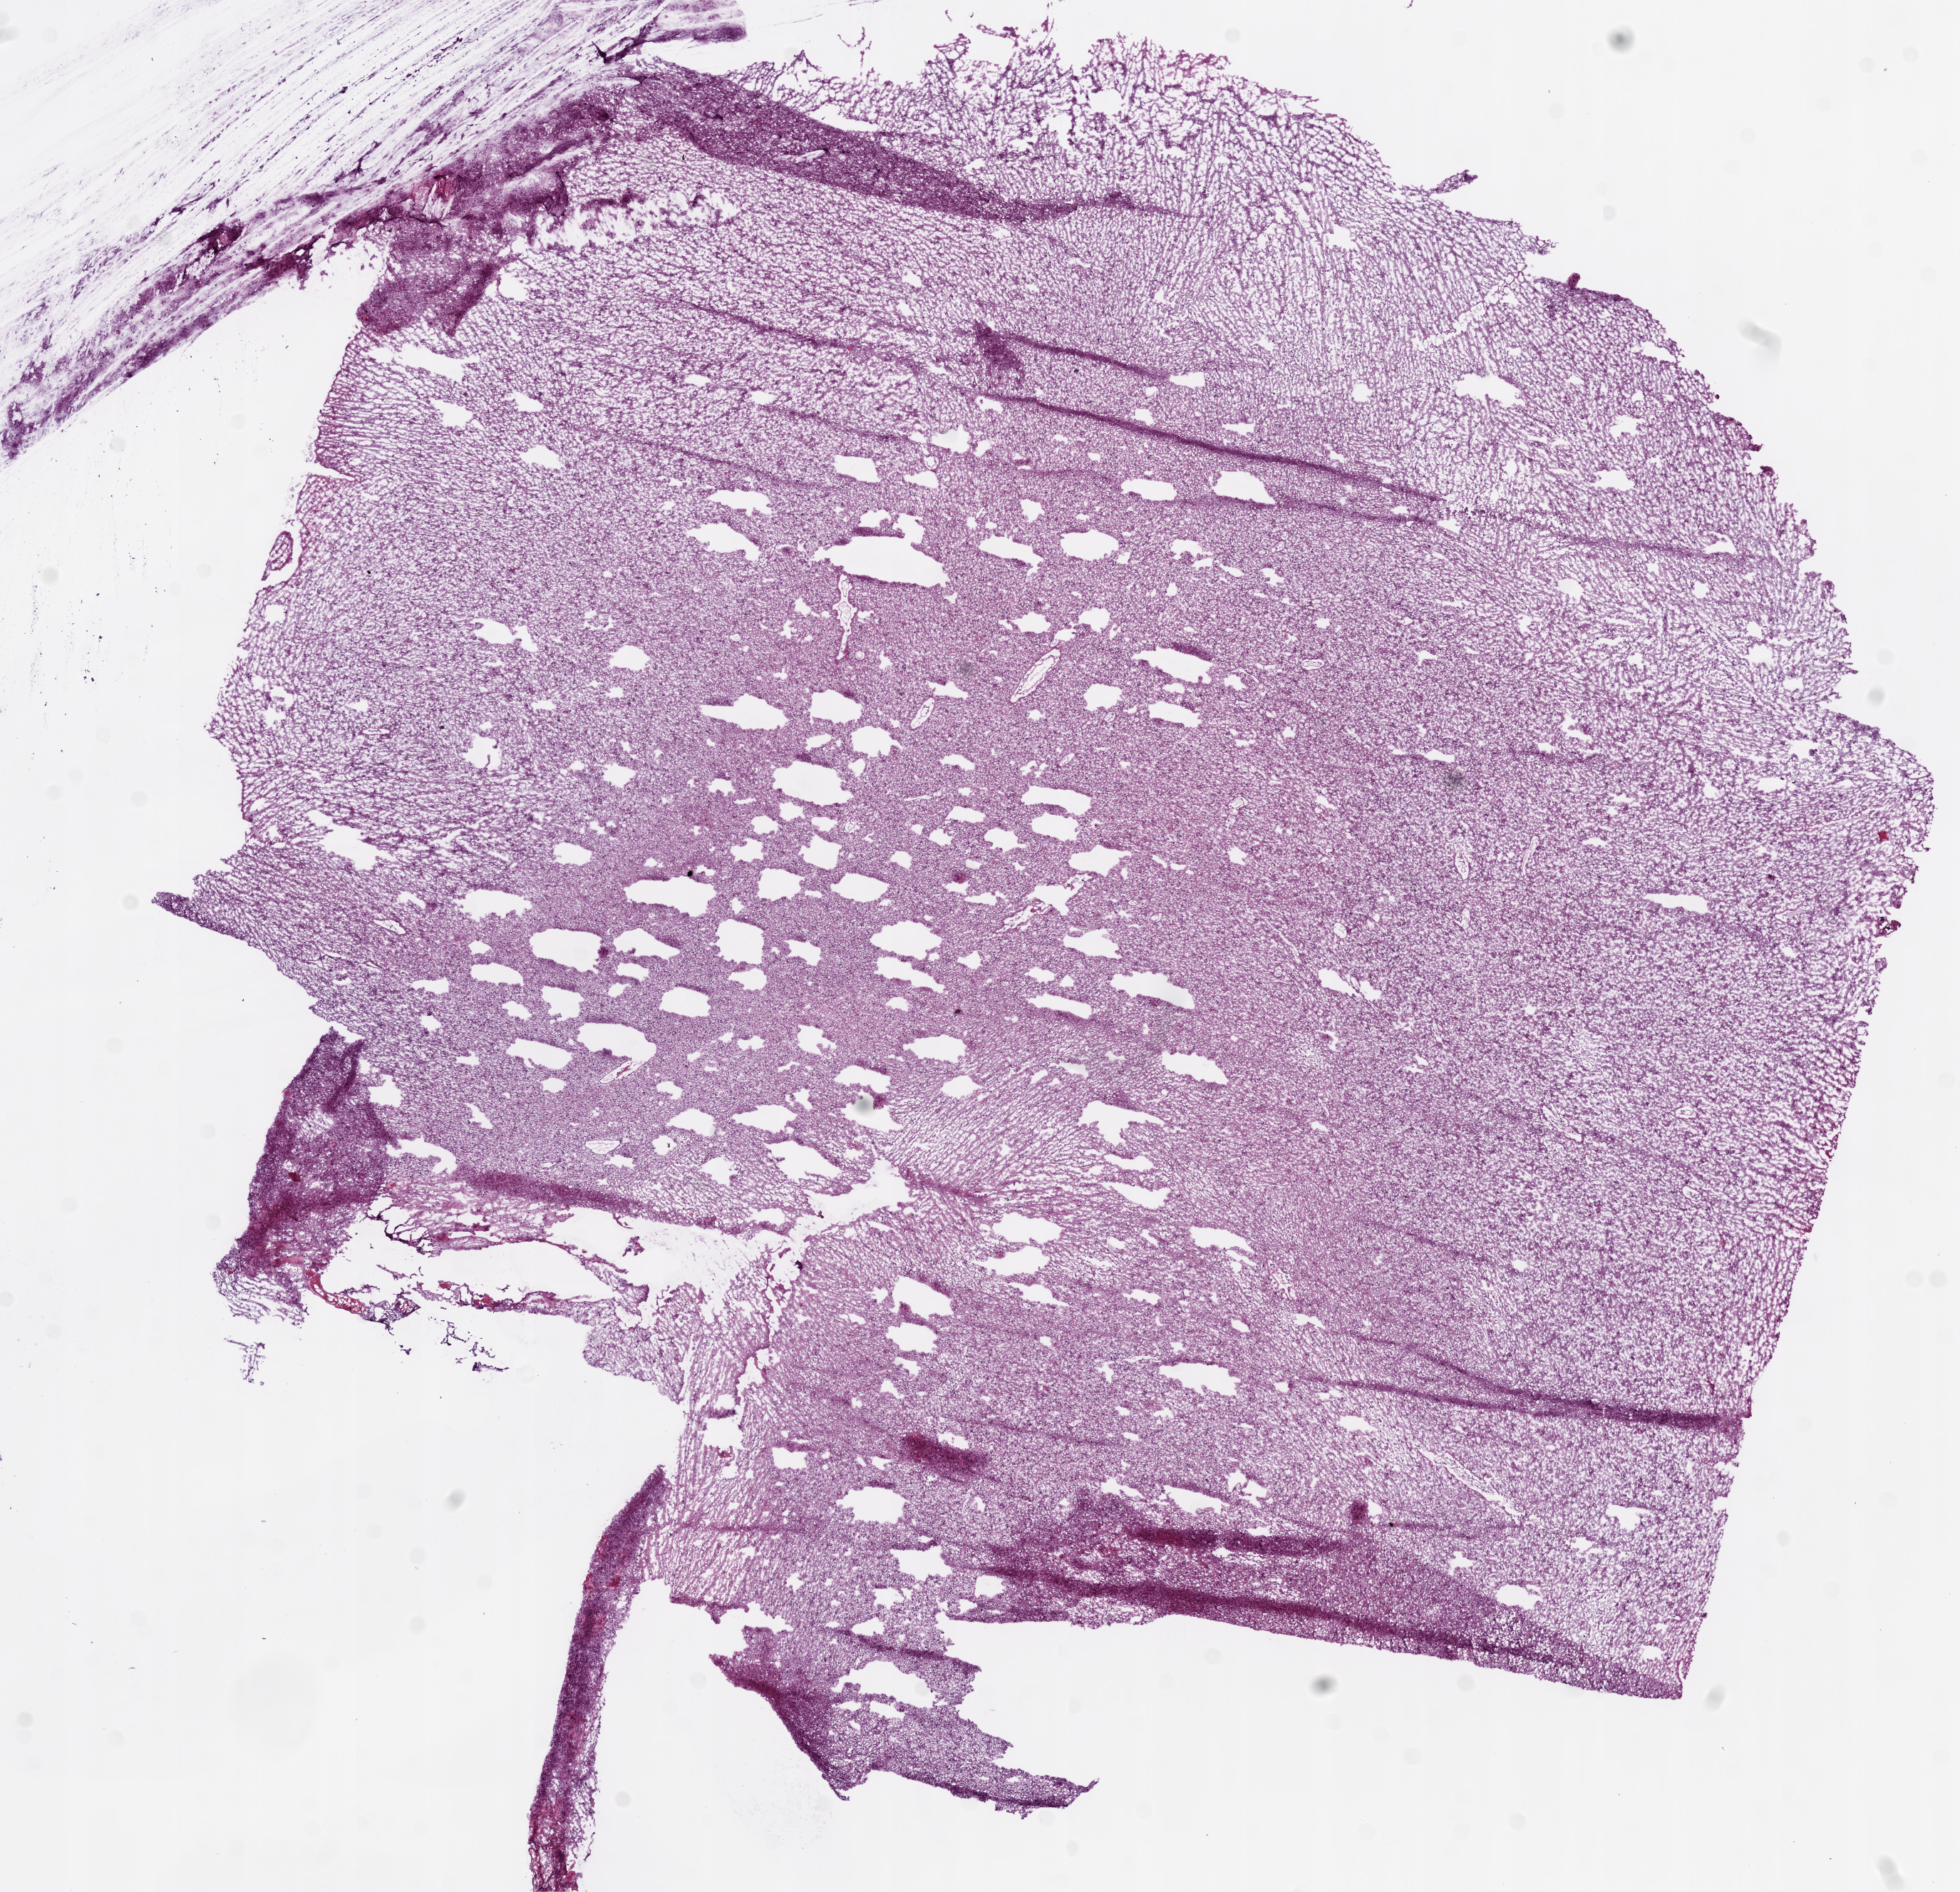
Digitized H&E tissue section (whole slide) — a low-resolution overview of the entire scanned area, about 11.0 x 10.6 mm. Frozen section from the bottom of the tissue portion. Sample: primary tumour, brain. Male patient; age at initial diagnosis 70 years. Pathologist review of this section (percent, as recorded): tumour cells 100%, tumour nuclei 80%, normal cells 0%, stromal cells 0%, necrosis 0%.
Histologic diagnosis: Glioblastoma.